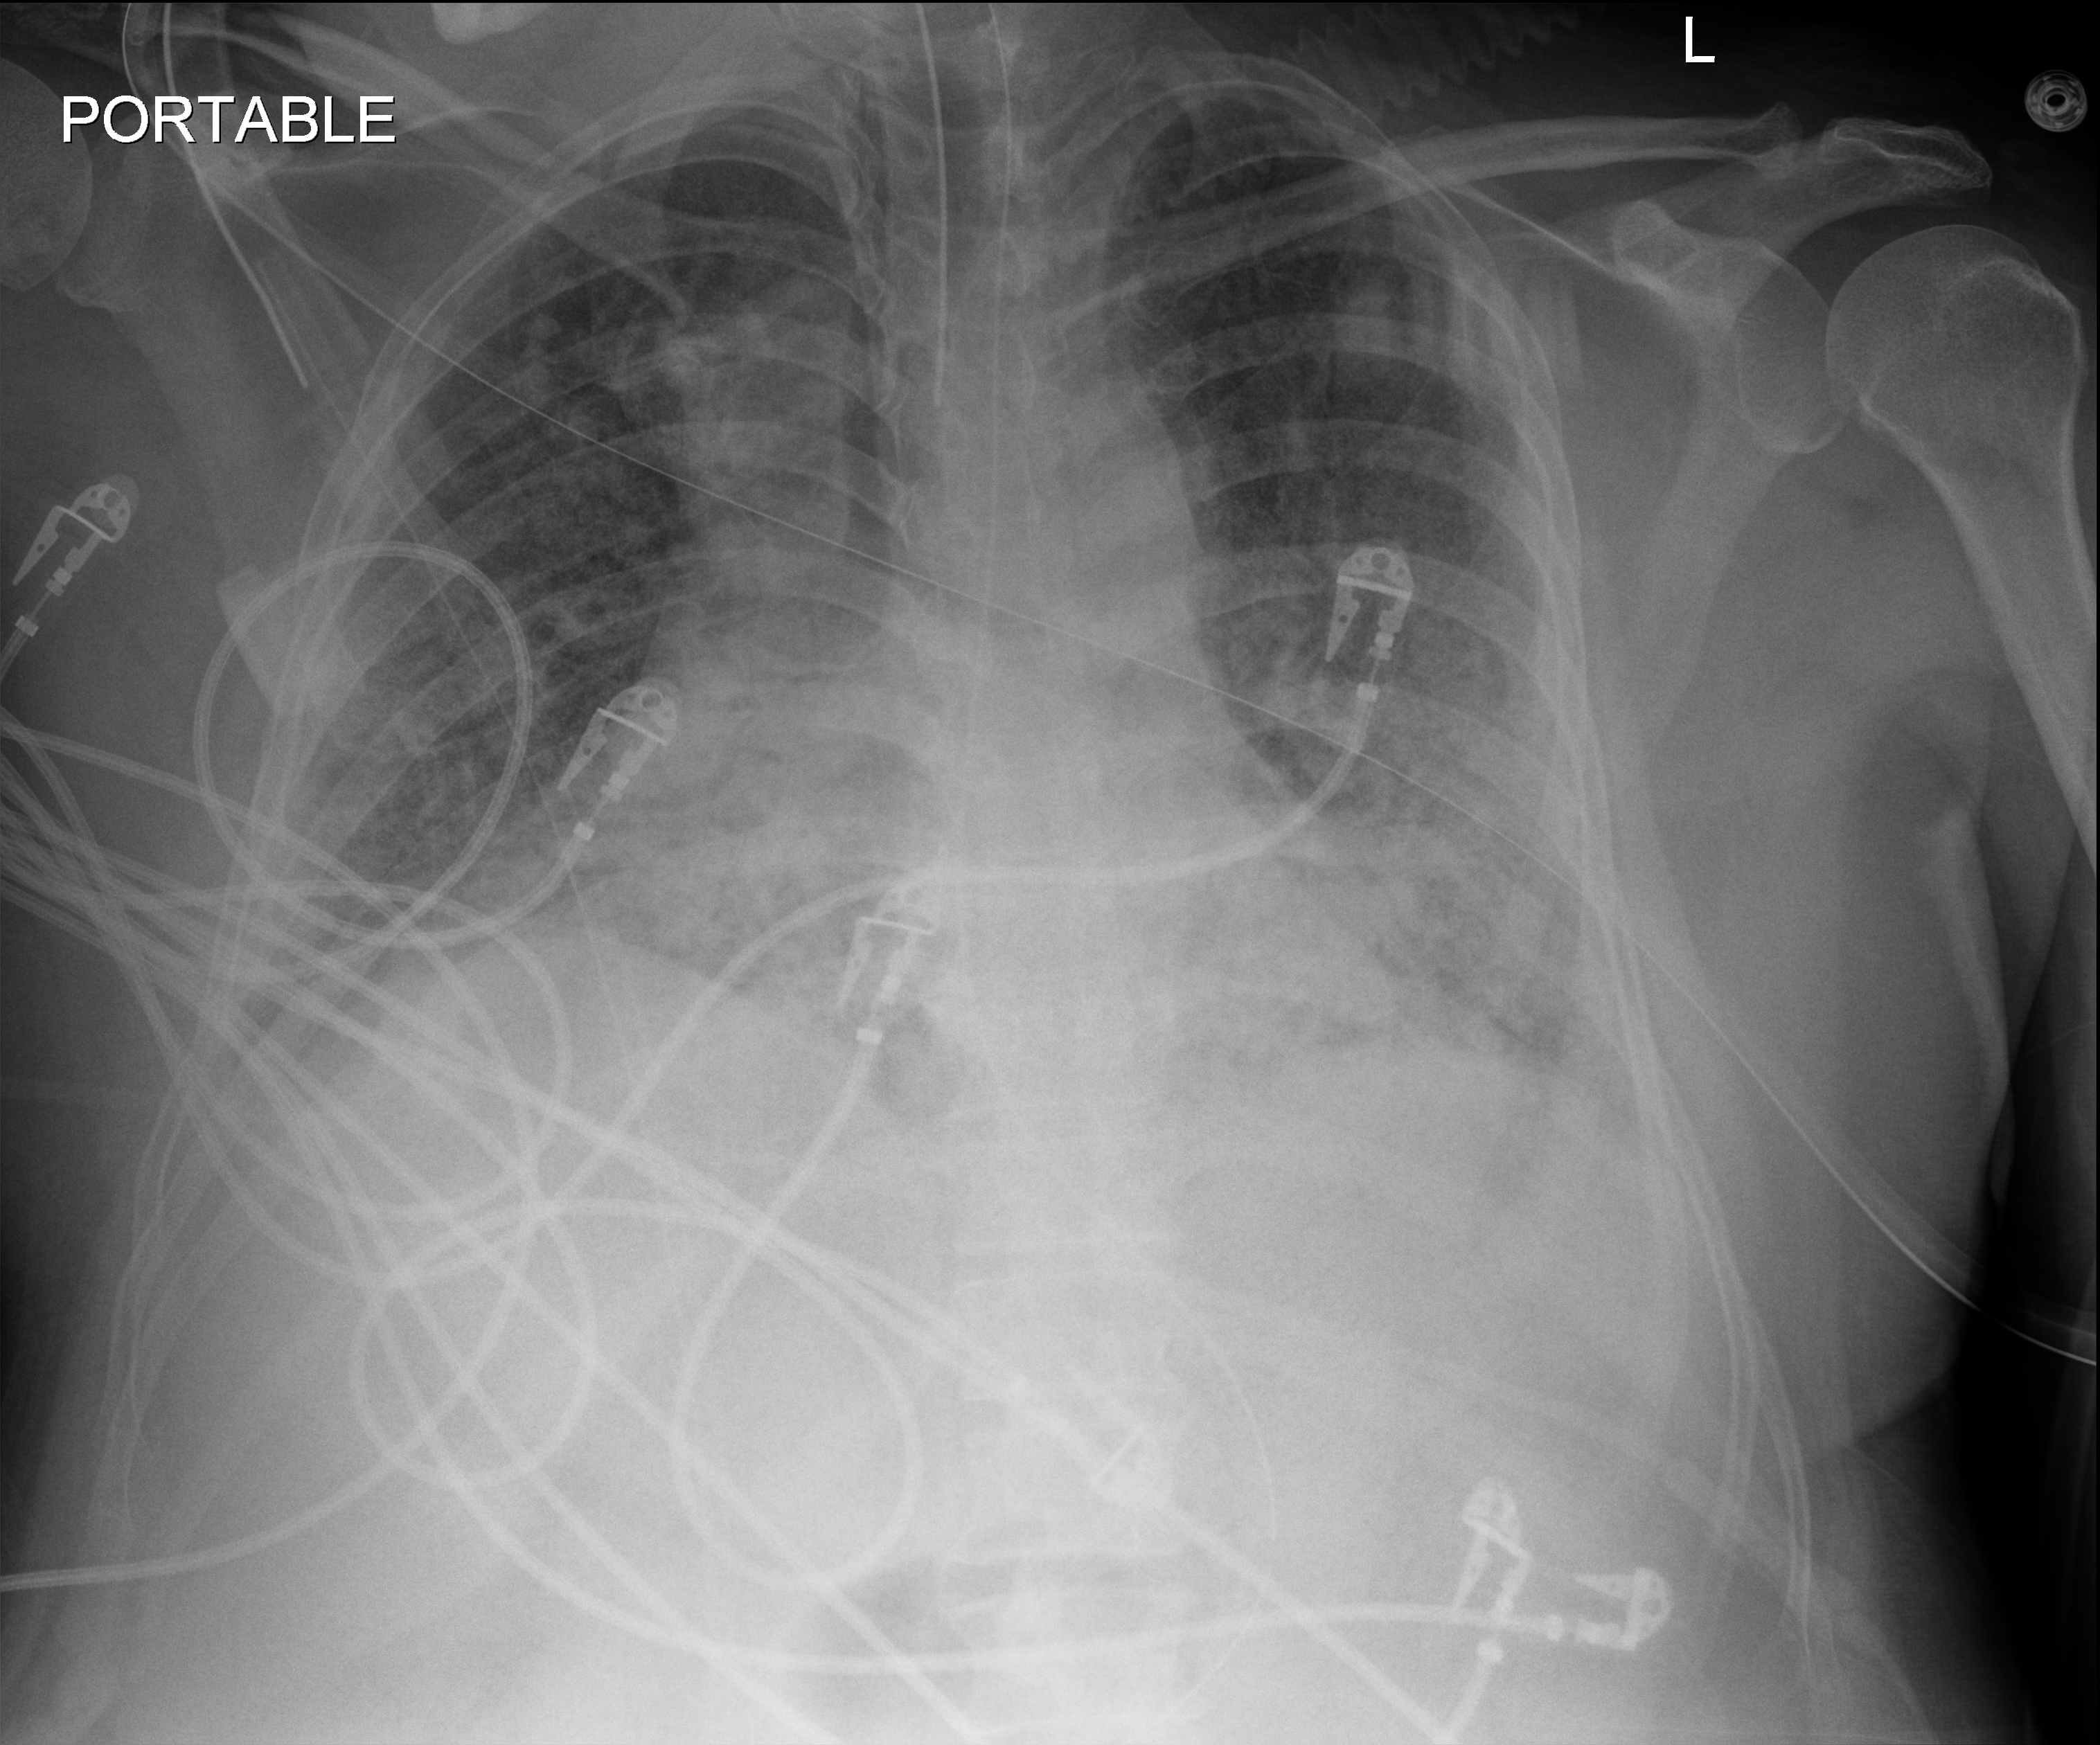
Bedside chest radiograph (digital radiography), anteroposterior (AP) projection. Adult patient hospitalised with COVID-19, age 18–59 years.
Admission-level facts for this patient (not findings on this image; timing relative to this image not recorded): mechanically ventilated during this hospital stay: yes; admitted to intensive care during this hospital stay: yes.